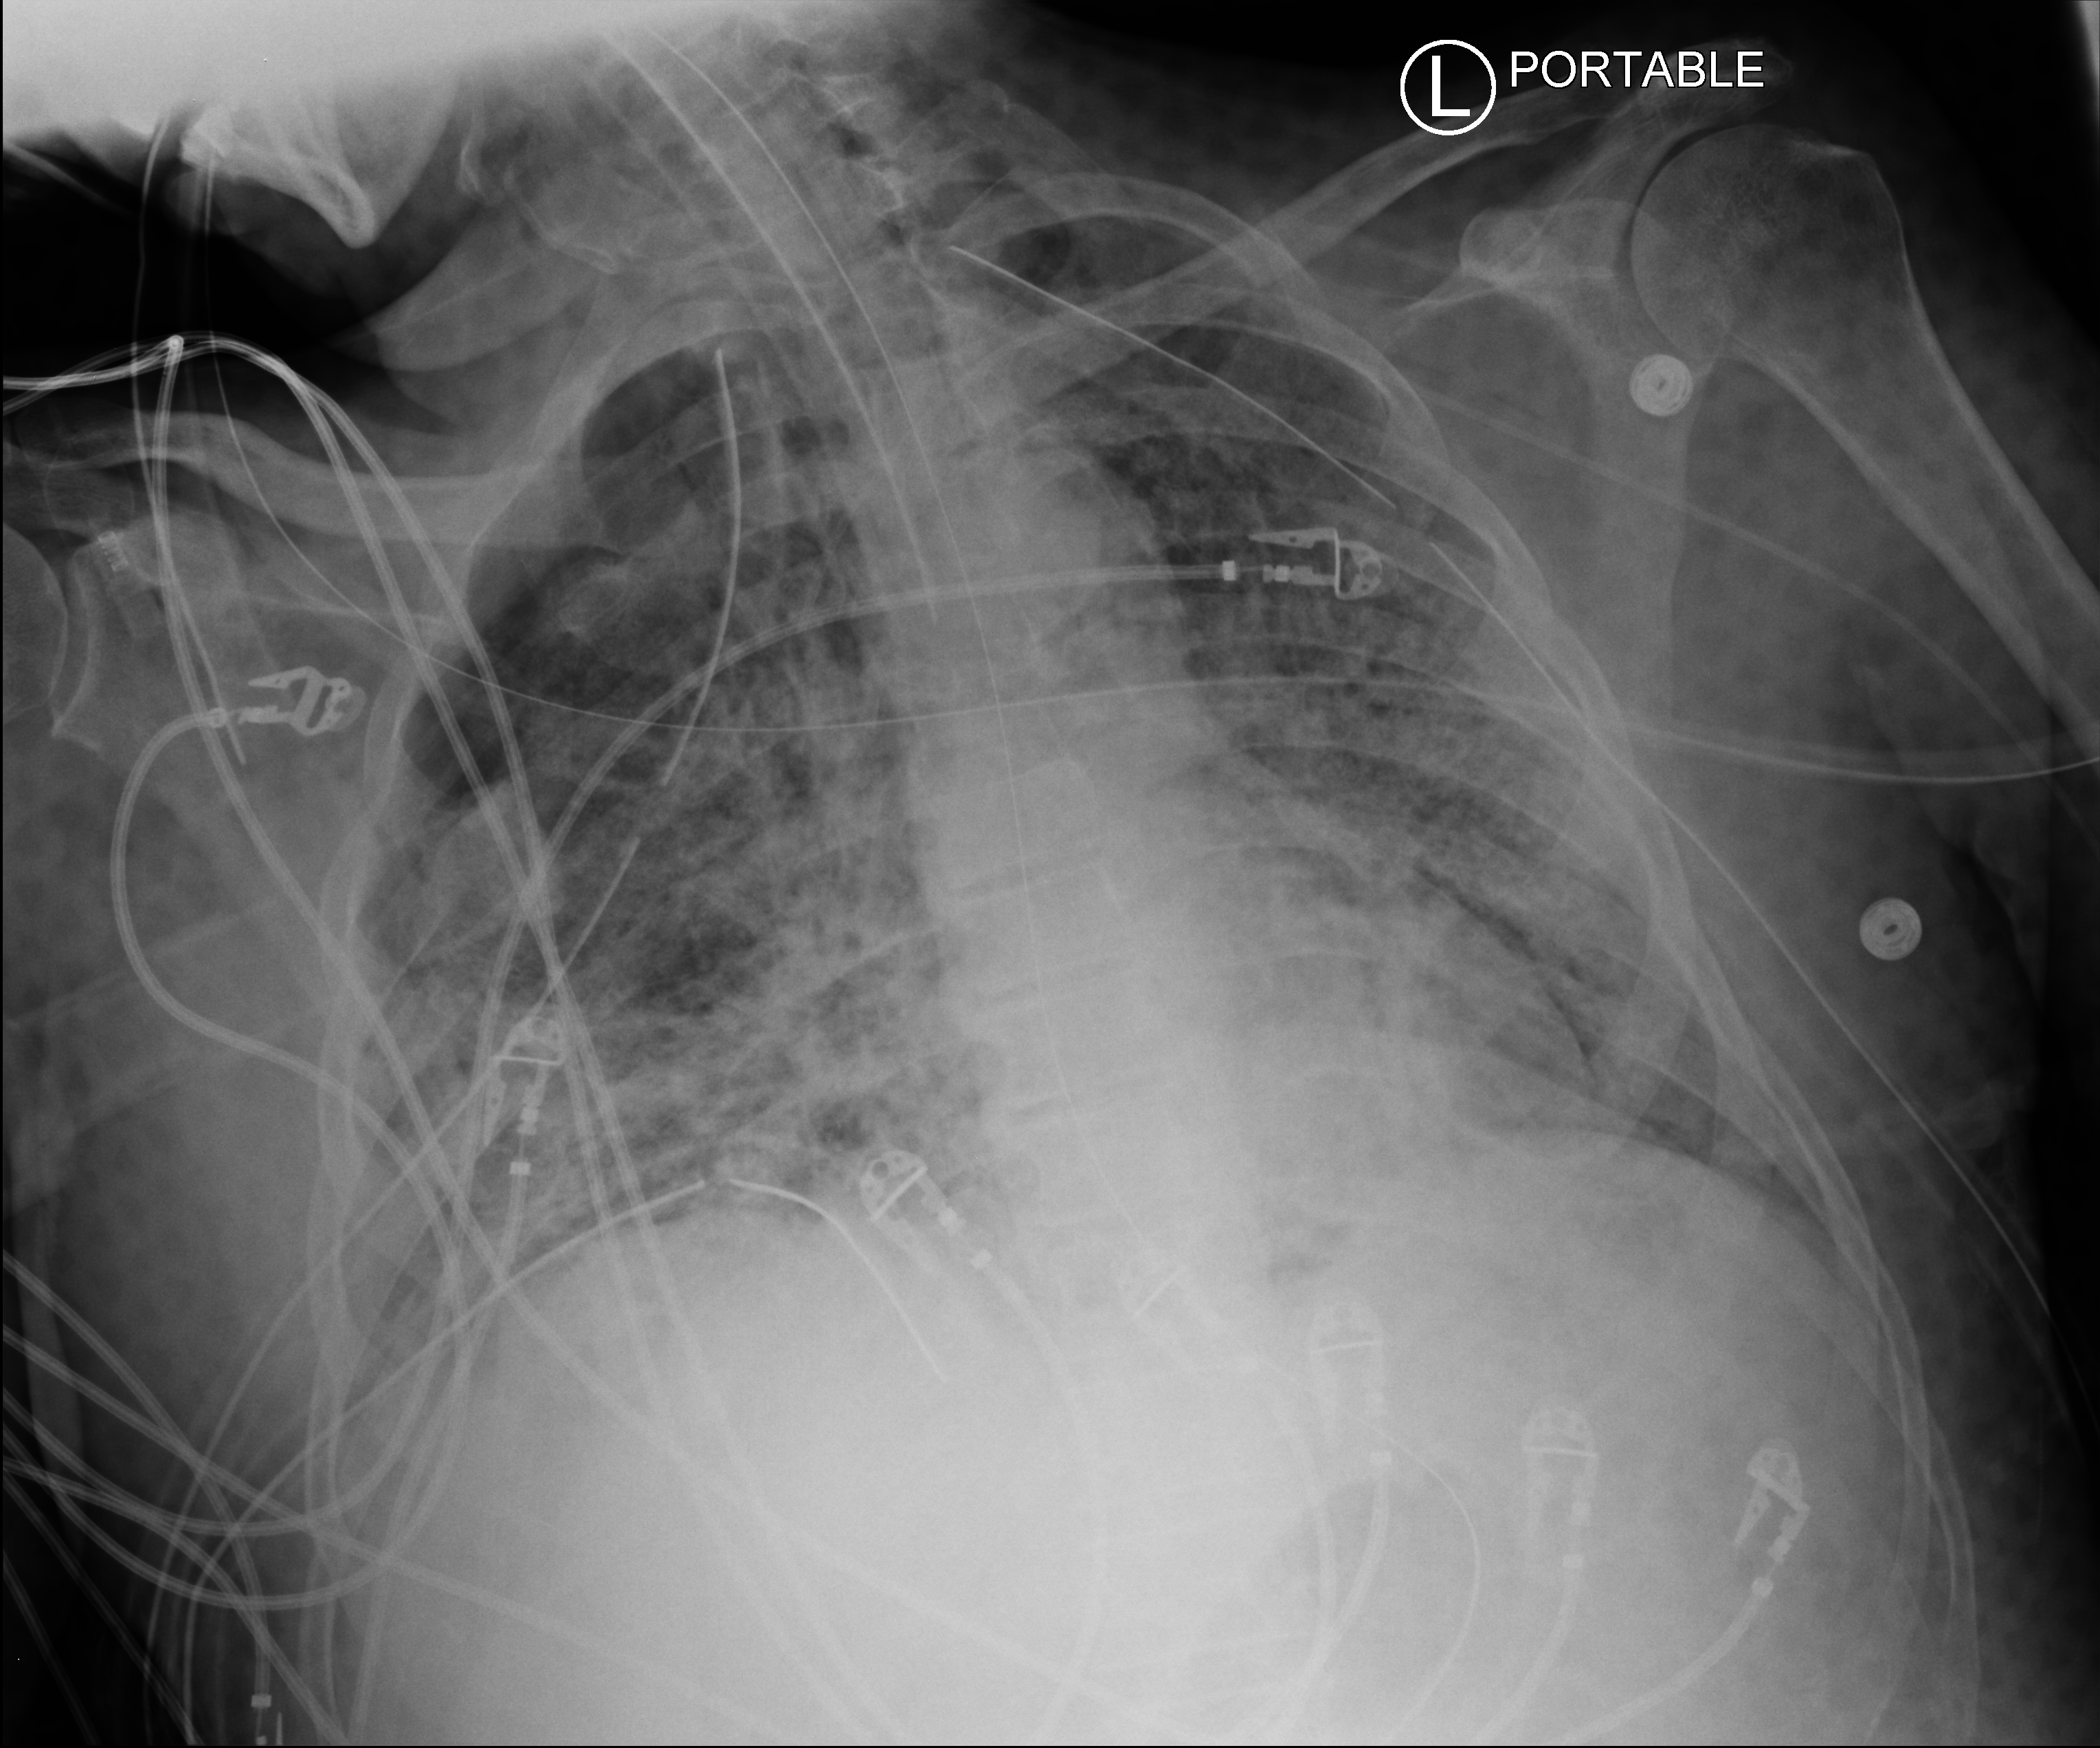
Bedside chest radiograph (computed radiography); anteroposterior (AP) projection. Male patient hospitalised with COVID-19, age 18–59 years.
From the hospital-stay record, not from the radiograph (when in the stay this image was taken is not recorded):
- mechanically ventilated during this hospital stay: yes
- admitted to intensive care during this hospital stay: yes